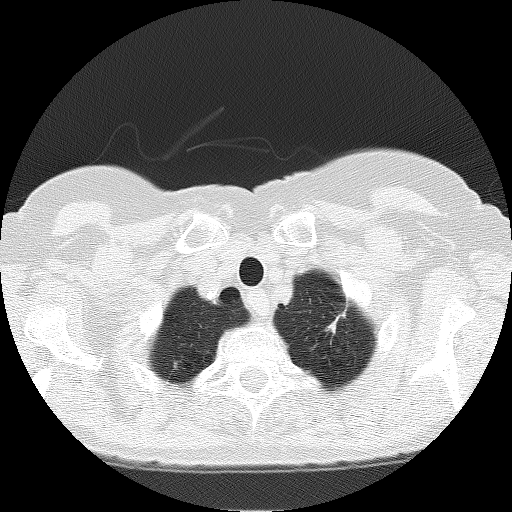
Low-dose screening chest CT, one axial slice. Slice 155 of 166 in the series (ordered by position). 120 kVp. Lung window (W 1500 / L -600 HU). 2 mm slice thickness. 512 × 512 image matrix, field of view 303 × 303 mm.
Outlined on this slice (expert manual segmentation):
- lesion 3 (nodule, upper lobe of left lung): bounding box [x1, y1, x2, y2] px = [328, 311, 345, 333]